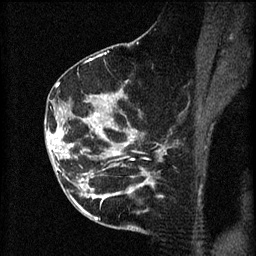
Breast MRI (dynamic contrast-enhanced), one sagittal slice; position 30 of 60 along the scan axis; 3 images stored at this slice position (order not interpretable as contrast timing); 1.5 T; TE 4.2 ms, TR 8.2 ms; 2 mm slice thickness; 256 × 256 image matrix, field of view 180 × 180 mm. Patient: female, 49 years.
Outlined on this slice (semi-automatically segmented with operator editing):
- analysis volume of interest (the breast-tissue region the enhancement analysis was run in; not a lesion): box from (x=45, y=126) to (x=105, y=177) px
- tumour enhancement mask (voxels above the 70 % enhancement threshold inside the analysis volume of interest): (x=47, y=126)–(x=105, y=159)